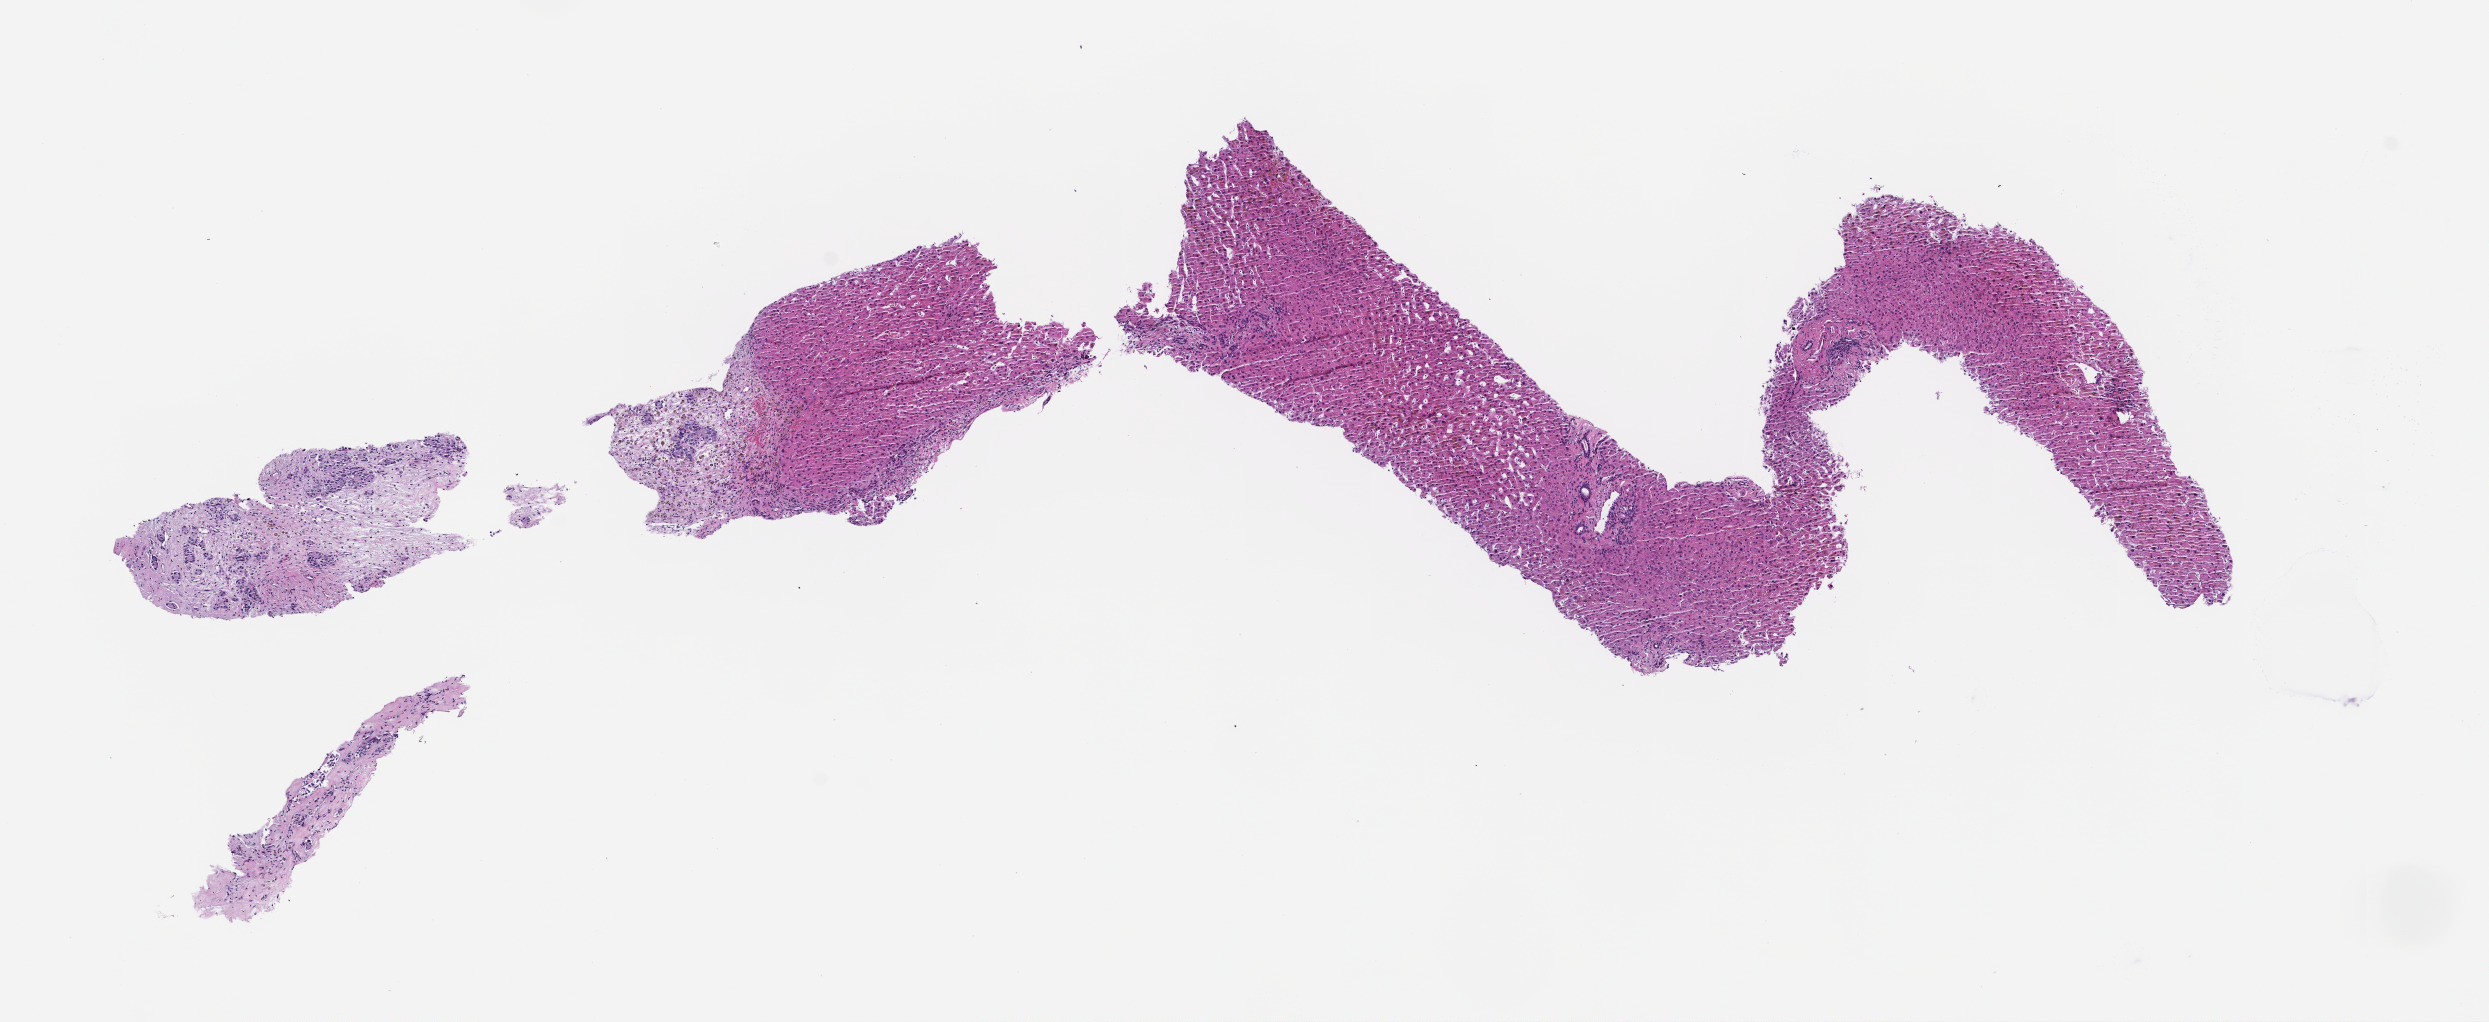
H&E whole-slide image — whole scanned area (about 10.1 x 4.1 mm) shown as a low-resolution overview. FFPE section. Specimen time point: collected at baseline (before treatment). Male patient.
This section: metastatic tumor tissue. Primary diagnosis of the patient: Prostate Carcinoma.